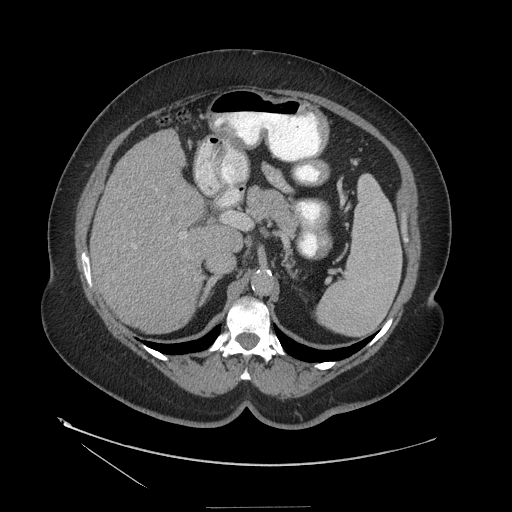
Contrast-enhanced abdominal CT (liver protocol), one axial slice. 140 kVp. Soft-tissue window (W 400 / L 40 HU). 2.5 mm slice thickness. 512 × 512 image matrix, field of view 480 × 480 mm. From the clinical record (not read from this slice): diagnosis: hepatocellular carcinoma (patient treated with transarterial chemoembolisation; whether this scan precedes or follows treatment is not stated here); TNM stage (as recorded): Stage-II; Child-Pugh class: A.
Structures marked on this image (semi-automatically segmented with operator editing):
- liver parenchyma outside the tumour (the mass and vessels are separate outlines, so this box may not span the whole liver): bounding box <90,130,212,332> (left, top, right, bottom; pixels)
- liver vessels: <134,246,136,248>